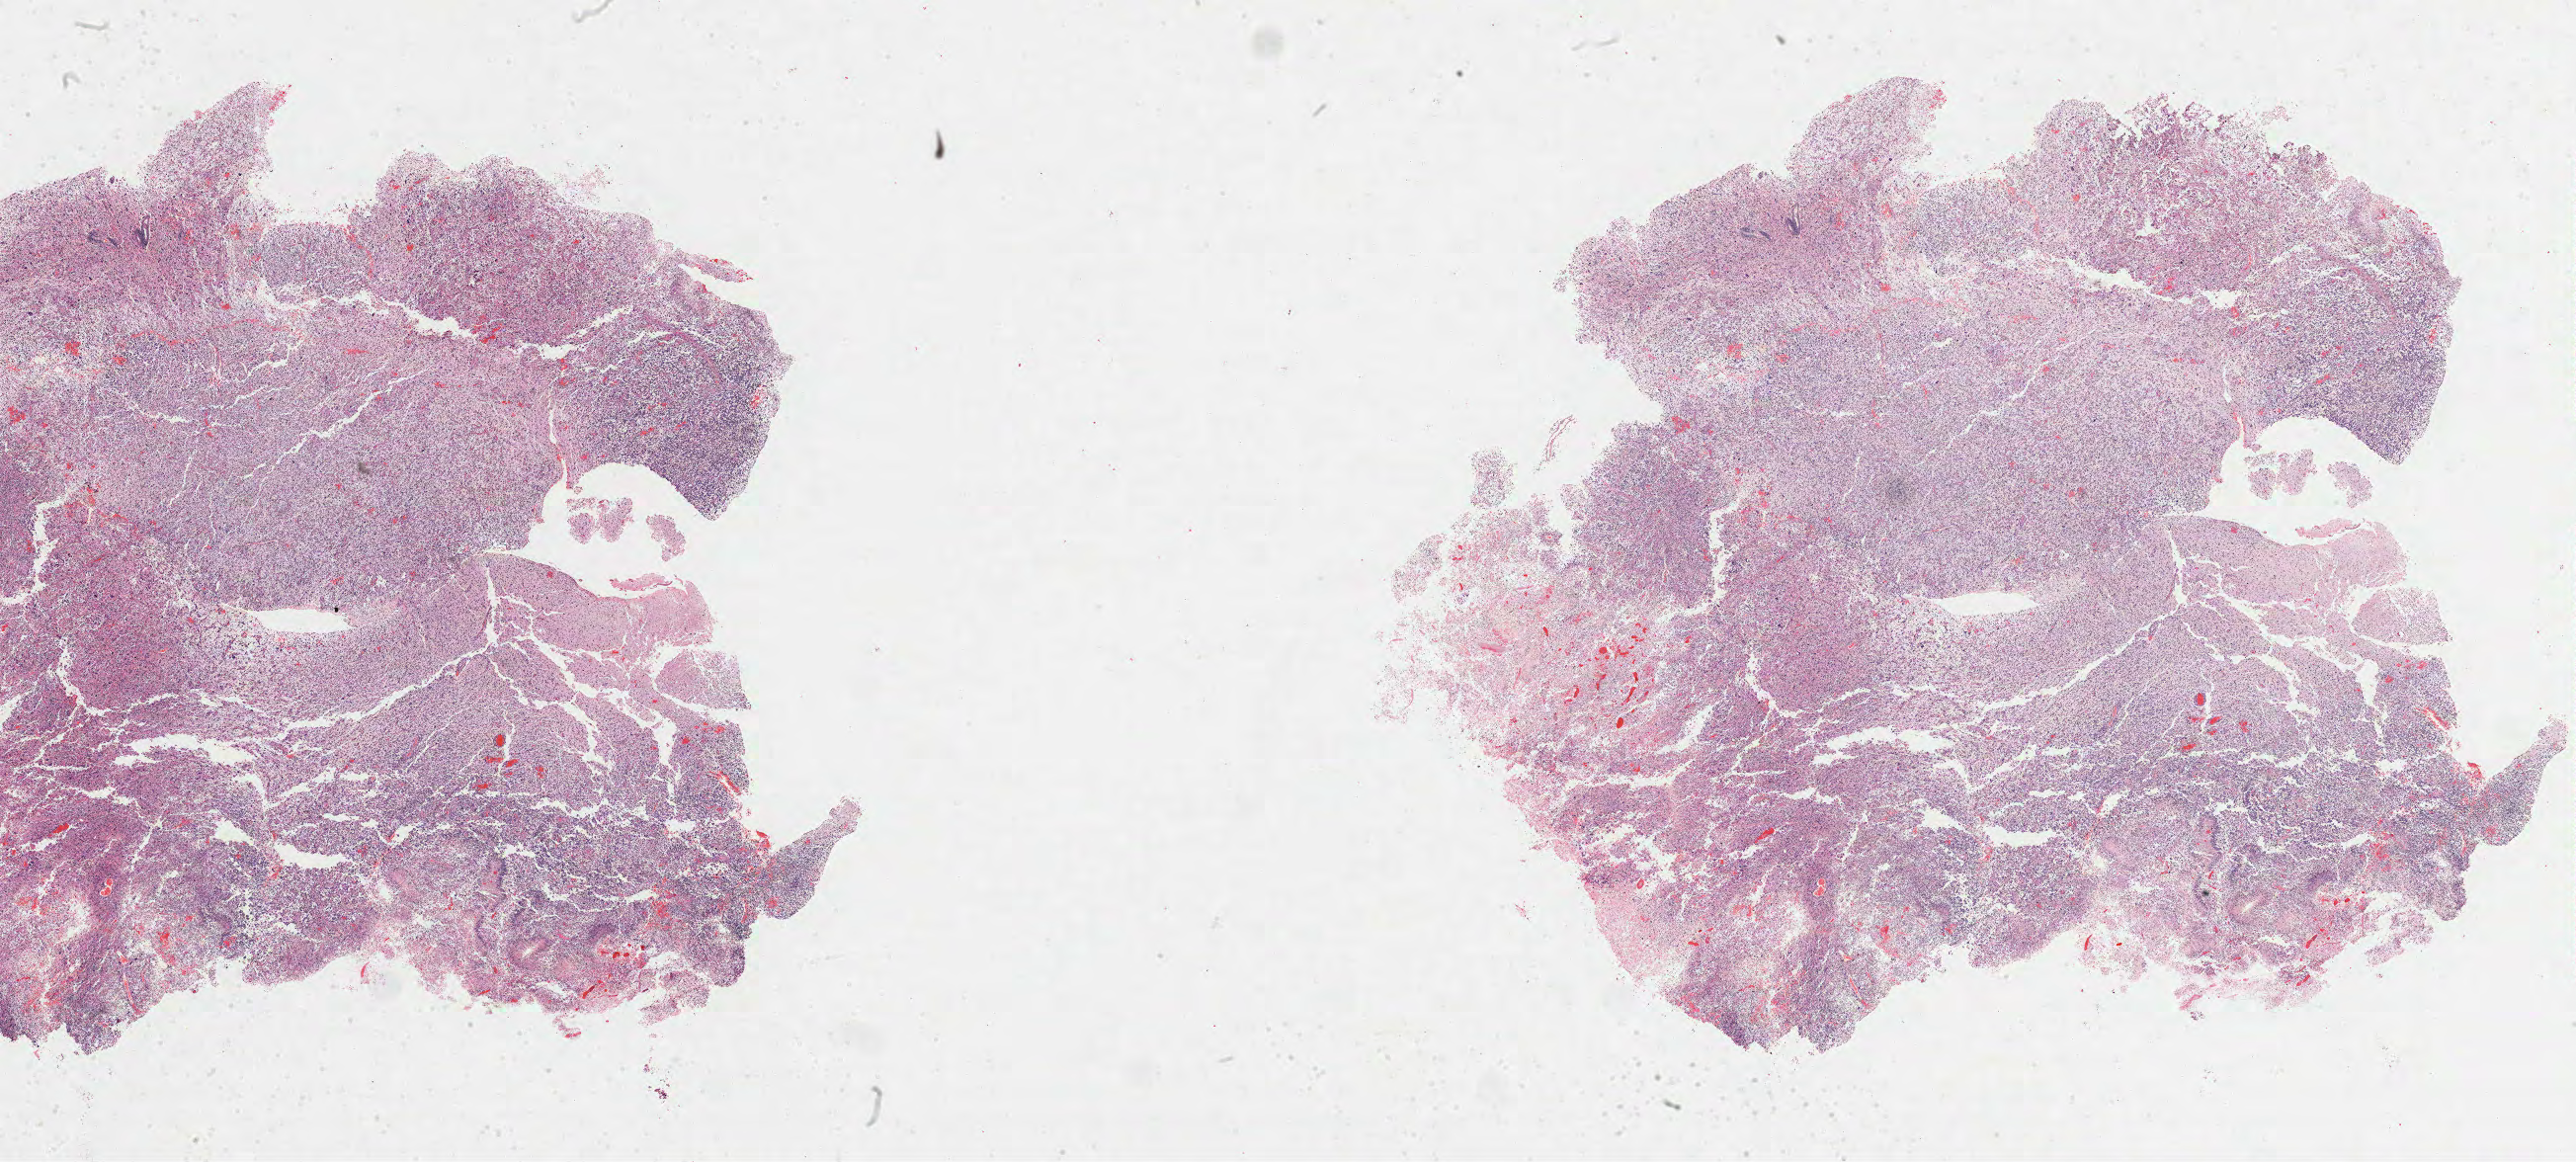
Whole-slide histology image, H&E-stained — whole scanned area (about 42.1 x 19.0 mm, slide scanned at 40x) shown as a low-resolution overview. FFPE section. Sample: primary tumour, brain. Patient: female, age at initial diagnosis 53 years.
Histologic diagnosis: Glioblastoma.